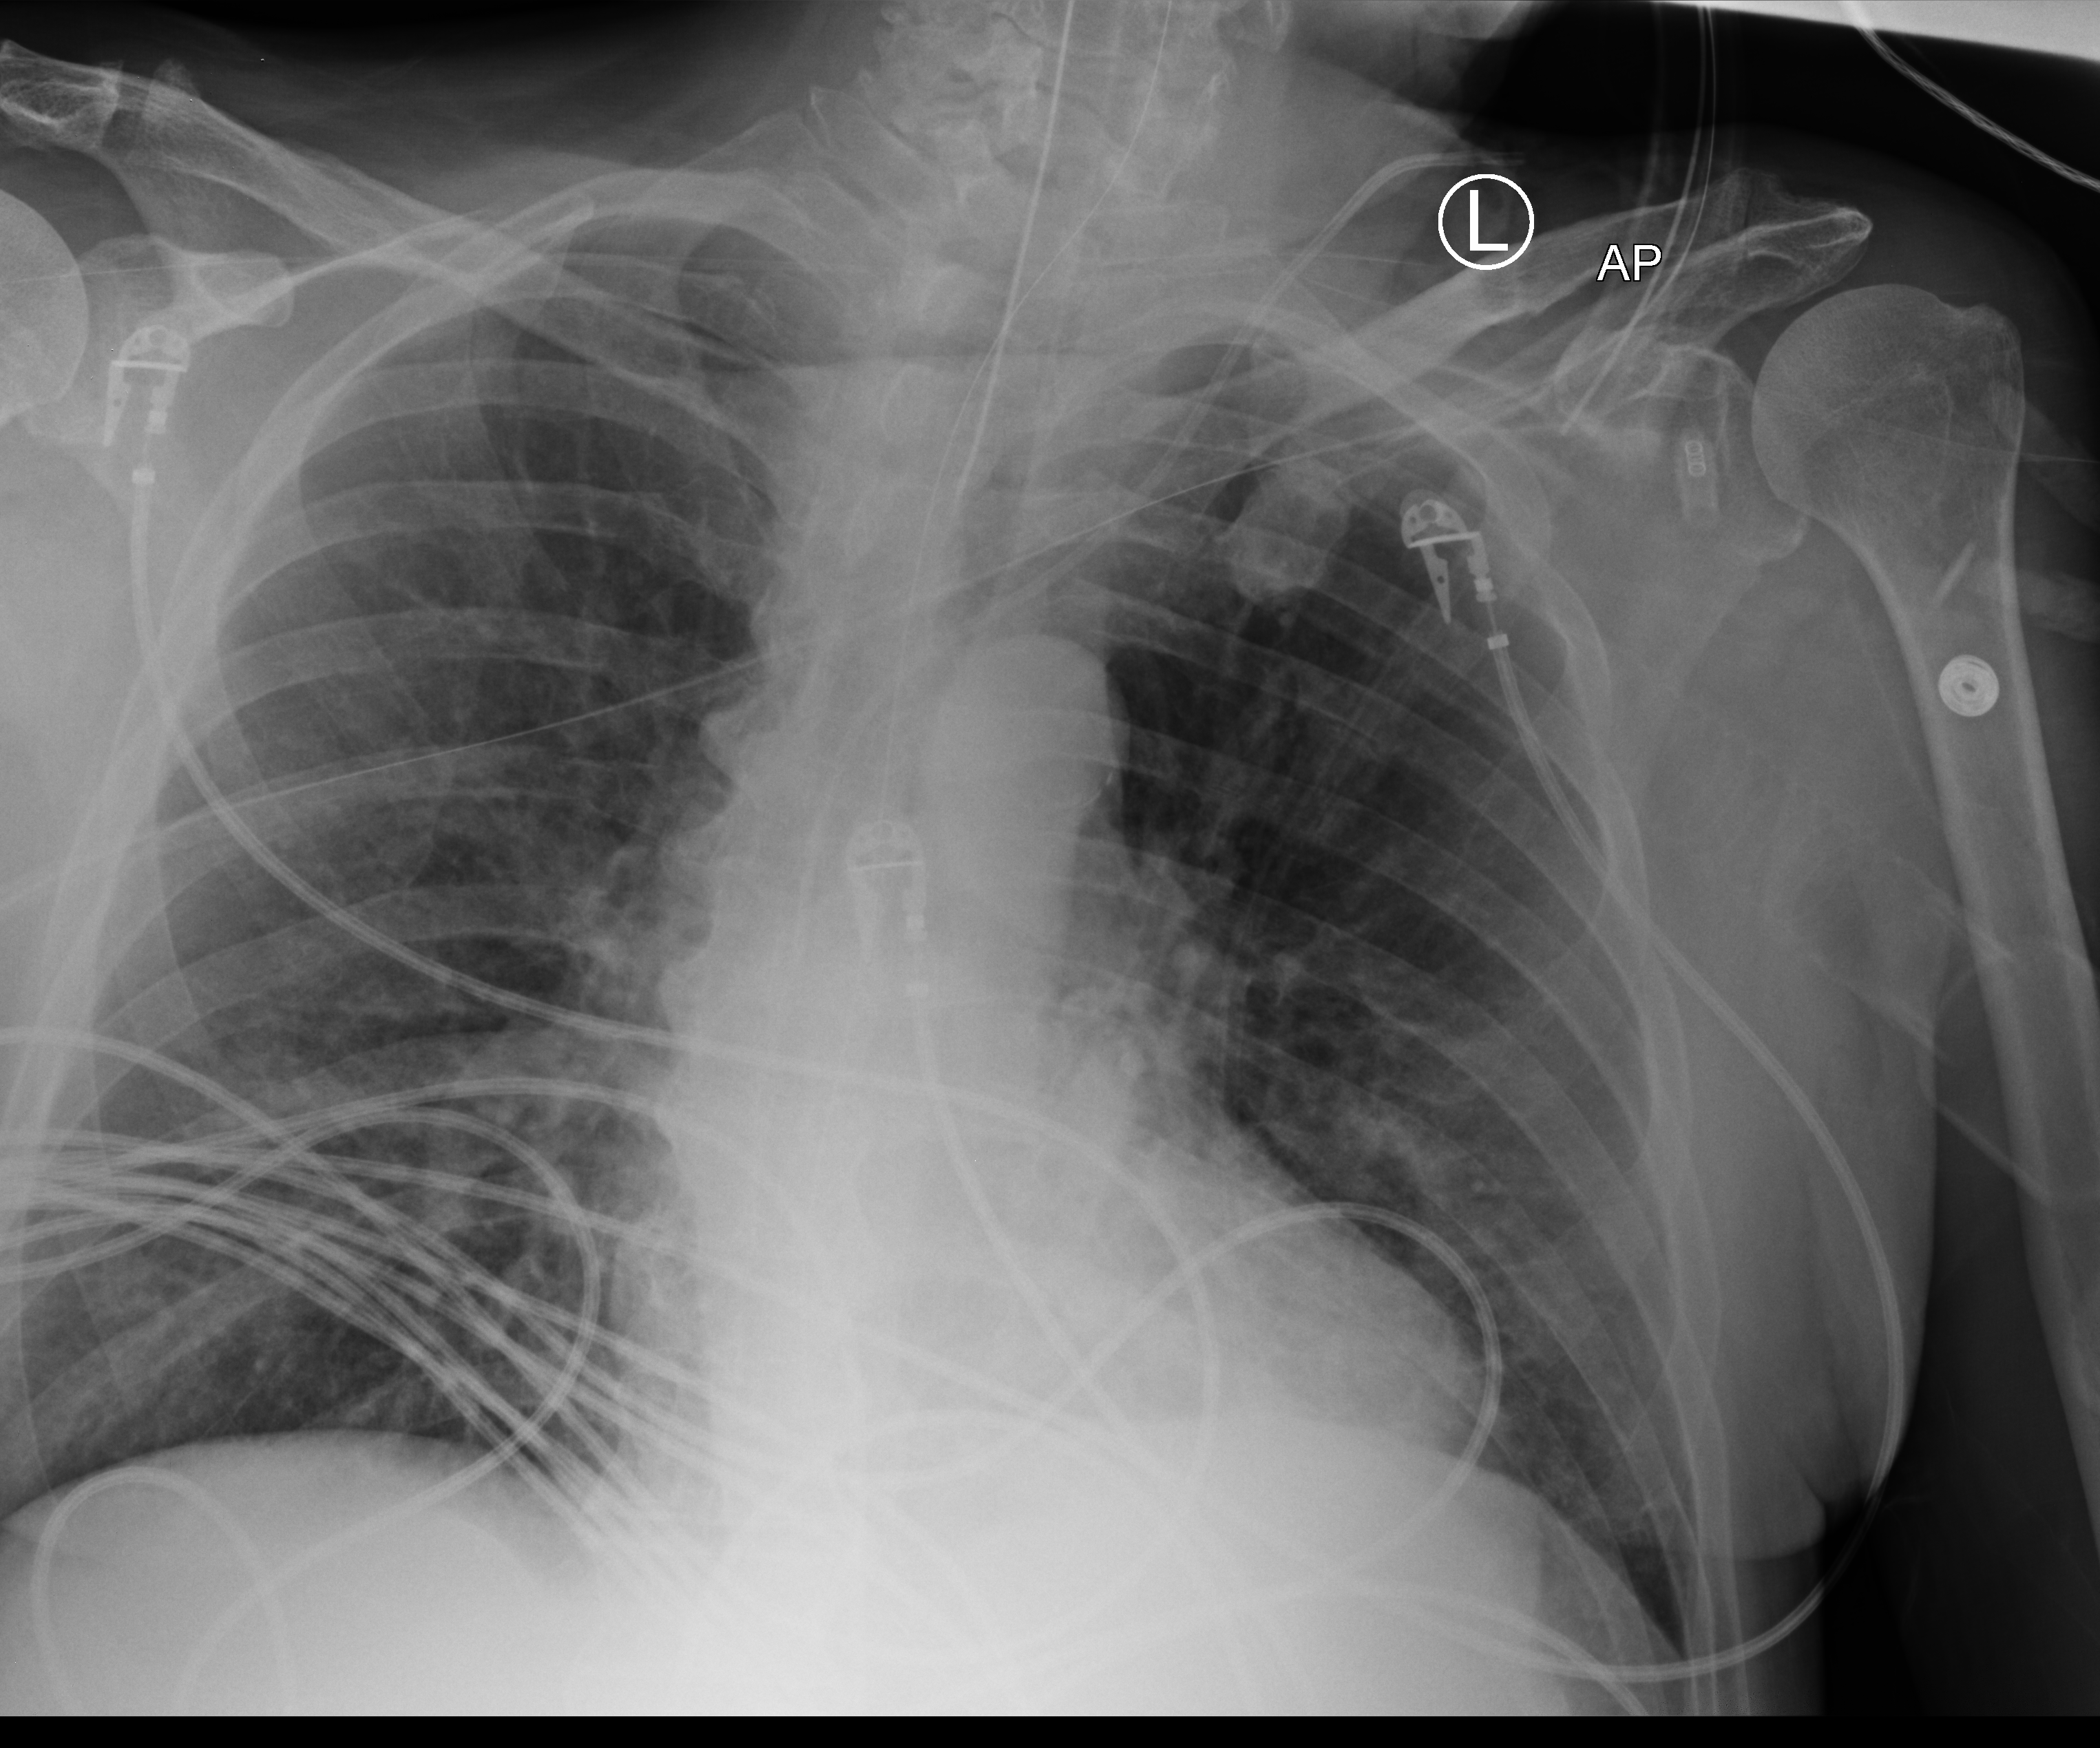
Bedside chest radiograph (computed radiography). Patient hospitalised with COVID-19; male, aged 60–74 years.
From the hospital-stay record, not from the radiograph (when in the stay this image was taken is not recorded):
- COPD (admission record): no